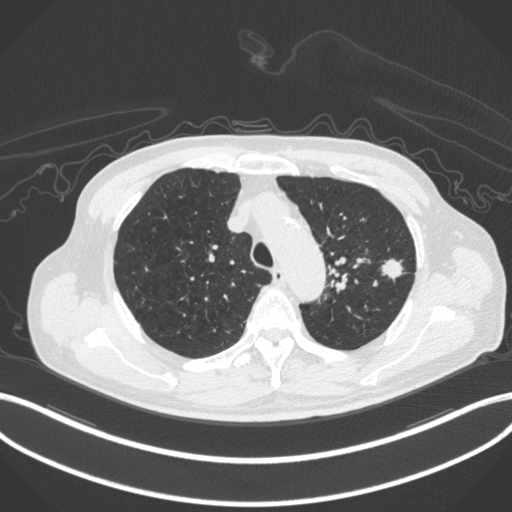
Chest CT, one axial slice; position 339 of 420 along the scan axis; lung window (W 1500 / L -600 HU); 512 × 512 image matrix. Patient: male, 77 years. From the clinical record (not read from this slice): clinical TNM (as recorded): T3 N1 M0.
Outlined on this slice (bounding box drawn by a radiologist):
- lung tumour (recorded histology: adenocarcinoma): bounding box [x1, y1, x2, y2] px = [376, 253, 408, 280]